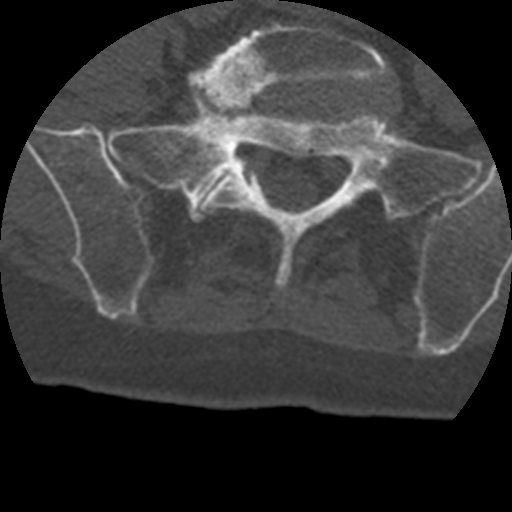
CT including the spine, one axial slice. Slice 31 of 399 in the series (ordered by position). Reconstruction kernel STANDARD. 120 kVp. Bone window (W 1800 / L 400 HU). 1.25 mm slice thickness. 512 × 512 image matrix. Patient age 69 years. From the clinical record (not read from this slice): primary cancer: prostate.
Annotated regions visible in this slice (semi-automatically segmented with operator editing):
- L5 vertebra: box from (x=190, y=23) to (x=392, y=212) px